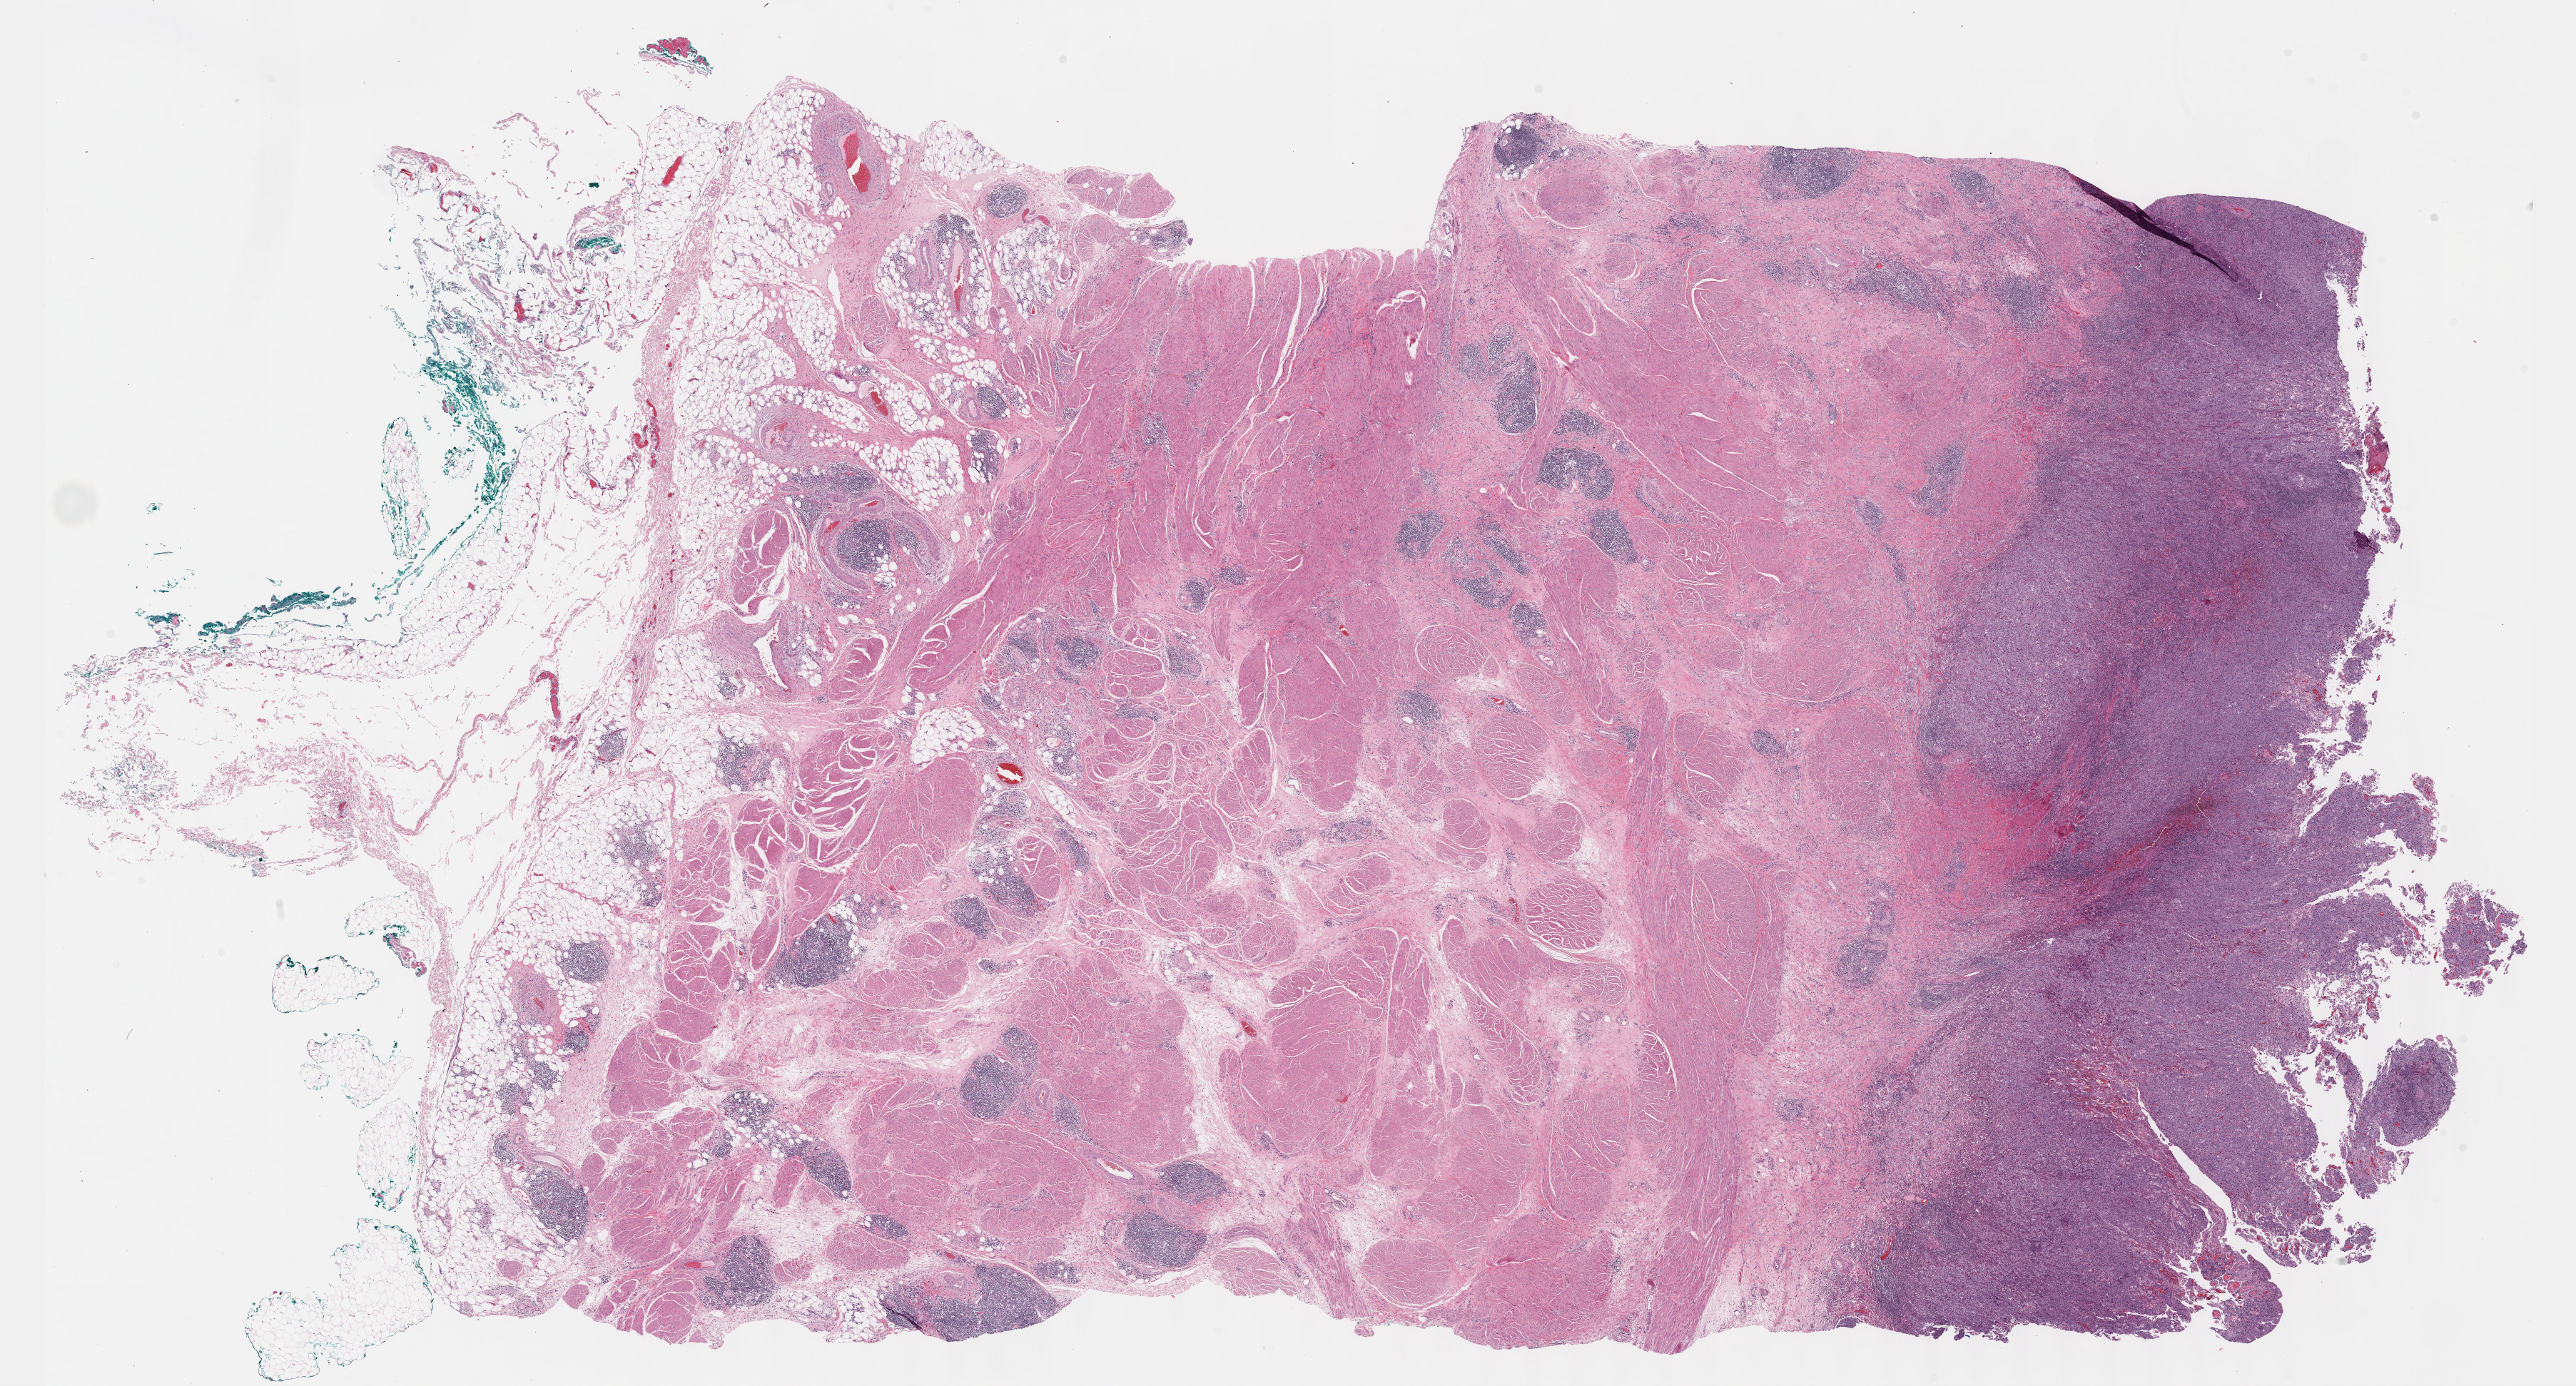
H&E whole-slide image — whole scanned area (about 29.2 x 15.7 mm) shown as a low-resolution overview; formalin-fixed paraffin-embedded (FFPE) diagnostic section; sample: primary tumour, bladder. Male, age 62 years at initial diagnosis. Histologic grade: high grade.
Lymph nodes positive (case pathology): 0 of 19 examined. AJCC pathologic stage: II (7th edition). Pathologic diagnosis: Transitional cell carcinoma.